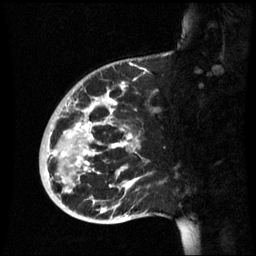
Breast MRI (dynamic contrast-enhanced), one sagittal slice; position 18 of 60 along the scan axis; dynamic contrast-enhanced series, image 2 of 3 at this slice position (ordered by acquisition); 1.5 T; TE 4.2 ms, TR 8.9 ms; 2.6 mm slice thickness; 256 × 256 image matrix, field of view 220 × 220 mm. Patient: female, 35 years. Case-level facts recorded for this patient, not image findings: setting: breast cancer imaged before/during neoadjuvant chemotherapy; receptor status: HR-positive, HER2-negative.
Outlined on this slice (semi-automatically segmented with operator editing):
- analysis volume of interest (the breast-tissue region the enhancement analysis was run in; not a lesion): box from (x=39, y=74) to (x=164, y=221) px
- tumour enhancement mask (voxels above the 70 % enhancement threshold inside the analysis volume of interest): (x=50, y=90)–(x=139, y=213)